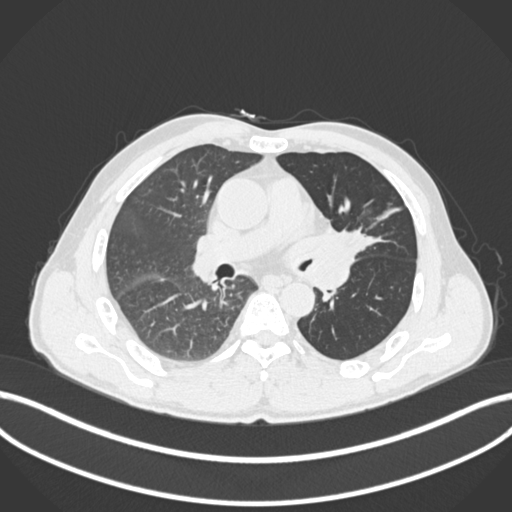
Chest CT, one axial slice; slice 104 of 255 in the series (ordered by position); lung window (W 1500 / L -600 HU); 512 × 512 image matrix. Patient: male, 57 years. Case-level facts recorded for this patient, not image findings: clinical TNM (as recorded): T2b N0 M0.
Outlined on this slice (rectangle marked by the reading radiologist):
- lung tumour (recorded histology: squamous cell carcinoma): bounding box (x1, y1, x2, y2) in pixels: (316, 227, 370, 261)